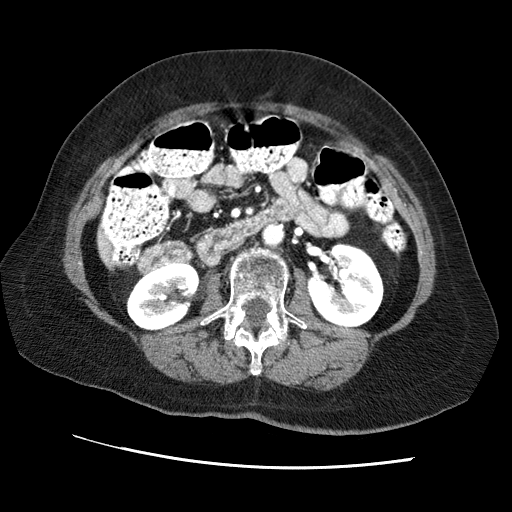
Contrast-enhanced abdominal CT (liver protocol), one axial slice. Position 11 of 65 along the scan axis. Reconstruction kernel STANDARD. Soft-tissue window (W 400 / L 40 HU). 2.5 mm slice thickness. 512 × 512 image matrix. From the clinical record (not read from this slice): diagnosis: hepatocellular carcinoma (patient treated with transarterial chemoembolisation; whether this scan precedes or follows treatment is not stated here); TNM stage (as recorded): Stage-II; Child-Pugh class: A; tumour nodularity: multinodular; tumour size: 2.5 cm.
Annotated regions visible in this slice (semi-automatically segmented with operator editing):
- liver parenchyma outside the tumour (the mass and vessels are separate outlines, so this box may not span the whole liver): box from (x=98, y=232) to (x=110, y=263) px